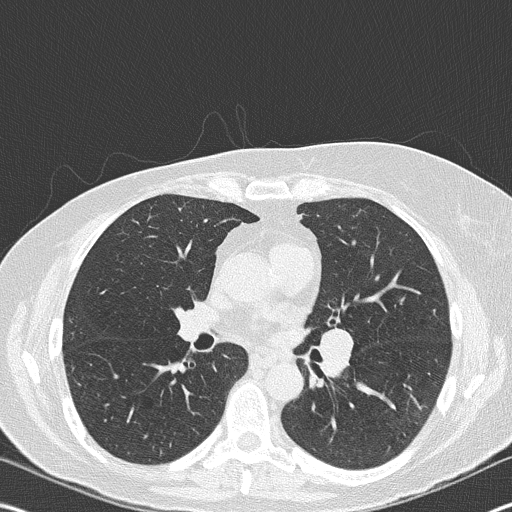
Low-dose screening chest CT, one axial slice; position 98 of 177 along the scan axis; 120 kVp; lung window (W 1500 / L -600 HU); 512 × 512 image matrix, field of view 342 × 342 mm.
Outlined on this slice (expert manual segmentation):
- lesion 2 (nodule, hilum of left lung): box from (x=319, y=329) to (x=353, y=376) px